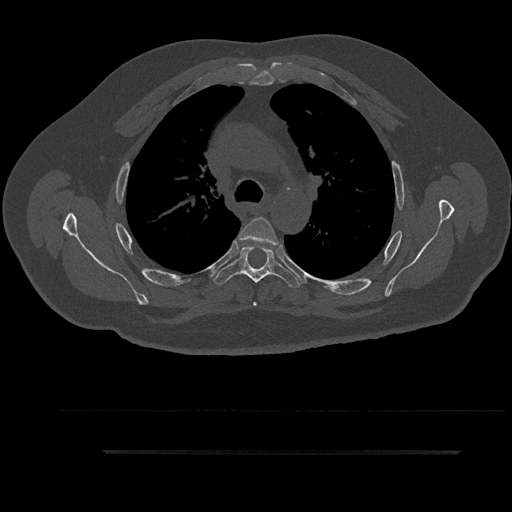
CT including the spine, one axial slice; position 644 of 797 along the scan axis; bone window (W 1800 / L 400 HU); 0.5 mm slice thickness; 512 × 512 image matrix, field of view 432 × 432 mm. Male patient, age 63 years. From the clinical record (not read from this slice): primary cancer: renal; vertebrae with lytic lesions (as recorded): T8.
Outlined on this slice (semi-automatically segmented with operator editing):
- T4 vertebra: bounding box [x1, y1, x2, y2] px = [238, 217, 281, 306]
- T5 vertebra: [215, 245, 299, 290]